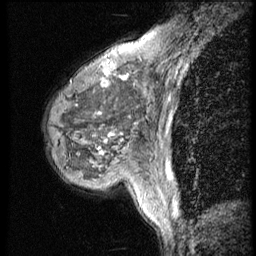
Breast MRI (dynamic contrast-enhanced), one sagittal slice; 4 images stored at this slice position (order not interpretable as contrast timing); 1.5 T; TE 4.2 ms, TR 9 ms; 2.5 mm slice thickness; 256 × 256 image matrix. Patient: female, 50 years. From the clinical record (not read from this slice): setting: breast cancer imaged before/during neoadjuvant chemotherapy; receptor status: triple-negative.
Structures marked on this image (semi-automatic segmentation, software-assisted and operator-edited):
- analysis volume of interest (the breast-tissue region the enhancement analysis was run in; not a lesion): box from (x=42, y=46) to (x=148, y=188) px
- tumour enhancement mask (voxels above the 140 % enhancement threshold inside the analysis volume of interest): (x=99, y=46)–(x=136, y=143)